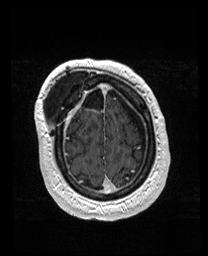
Brain MRI from a brain-tumour surgery series, one axial slice. Slice 37 of 176 in the series (ordered by position). T1-weighted post-contrast. 1 mm slice thickness. 208 × 256 image matrix, field of view 208 × 256 mm. From the clinical record (not read from this slice): histopathology: Astrocytoma; WHO grade: 4; IDH mutation: yes.
Structures marked on this image (expert manual segmentation):
- previous resection cavity: bounding box <57,85,78,108> (left, top, right, bottom; pixels)